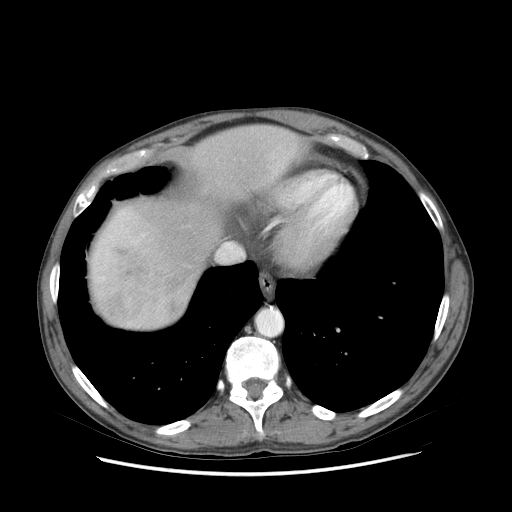
Contrast-enhanced abdominal CT (liver protocol), one axial slice; position 71 of 89 along the scan axis; soft-tissue window (W 400 / L 40 HU); 2.5 mm slice thickness; 512 × 512 image matrix. From the clinical record (not read from this slice): diagnosis: hepatocellular carcinoma (patient treated with transarterial chemoembolisation; whether this scan precedes or follows treatment is not stated here); TNM stage (as recorded): Stage-IIIB; Child-Pugh class: A; tumour differentiation: moderately differentiated; tumour nodularity: multinodular.
Annotated regions visible in this slice (semi-automatically segmented with operator editing):
- abdominal aorta: bounding box (x1, y1, x2, y2) in pixels: (258, 309, 281, 336)
- liver parenchyma outside the tumour (the mass and vessels are separate outlines, so this box may not span the whole liver): (90, 126, 302, 328)
- liver vessels: (94, 210, 145, 325)